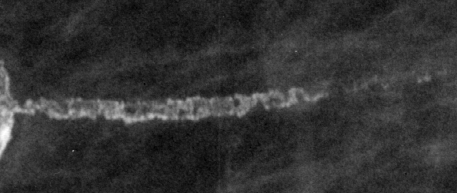
Crop from a digitized film mammogram around one marked abnormality; right breast; MLO view; BI-RADS breast density category 1 (scale 1–4).
Finding: calcifications, morphology vascular; BI-RADS assessment category 2; subtlety rating 4 on a 1 (subtle) to 5 (obvious) scale; benign; no additional work-up was recommended (benign without callback).